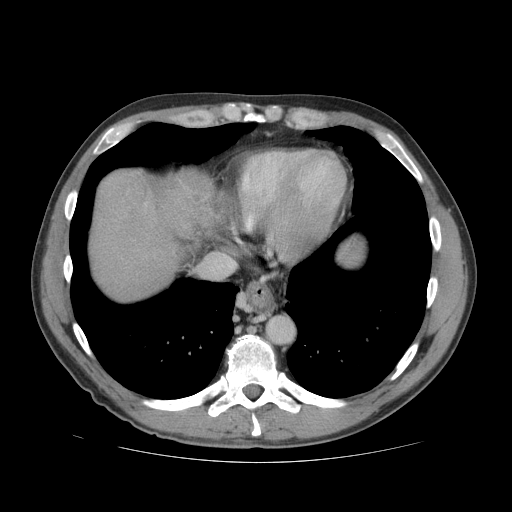
Contrast-enhanced abdominal CT (liver protocol), one axial slice. Reconstruction kernel STANDARD. Soft-tissue window (W 400 / L 40 HU). 2.5 mm slice thickness. 512 × 512 image matrix. Case-level facts recorded for this patient, not image findings: diagnosis: hepatocellular carcinoma (patient treated with transarterial chemoembolisation; whether this scan precedes or follows treatment is not stated here); TNM stage (as recorded): Stage-IVB; Child-Pugh class: B; tumour differentiation: well differentiated; tumour nodularity: multinodular.
Structures marked on this image (semi-automatic segmentation, software-assisted and operator-edited):
- liver parenchyma outside the tumour (the mass and vessels are separate outlines, so this box may not span the whole liver): box from (x=88, y=168) to (x=212, y=300) px
- mass: (x=99, y=169)–(x=147, y=219)